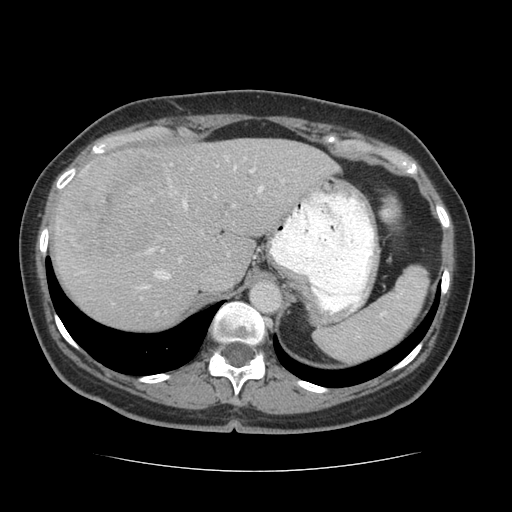
Contrast-enhanced abdominal CT (liver protocol), one axial slice; slice 48 of 75 in the series (ordered by position); reconstruction kernel STANDARD; soft-tissue window (W 400 / L 40 HU); 2.5 mm slice thickness; 512 × 512 image matrix, field of view 360 × 360 mm. From the clinical record (not read from this slice): diagnosis: hepatocellular carcinoma (patient treated with transarterial chemoembolisation; whether this scan precedes or follows treatment is not stated here); TNM stage (as recorded): Stage-I; Child-Pugh class: A.
Structures marked on this image (semi-automatically segmented with operator editing):
- liver parenchyma outside the tumour (the mass and vessels are separate outlines, so this box may not span the whole liver): box from (x=52, y=138) to (x=338, y=330) px
- mass: (x=59, y=149)–(x=181, y=257)
- liver vessels: (x=58, y=156)–(x=285, y=299)